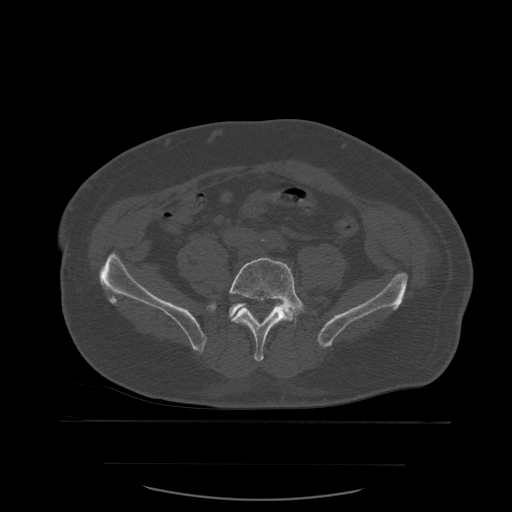
CT including the spine, one axial slice. Bone window (W 1800 / L 400 HU). 512 × 512 image matrix, field of view 479 × 479 mm. Patient age 71 years. Case-level facts recorded for this patient, not image findings: primary cancer: lung; vertebrae with lytic lesions (as recorded): T1, T2, L5, S1.
Structures marked on this image (semi-automatically segmented with operator editing):
- L5 vertebra: bounding box (x1, y1, x2, y2) in pixels: (229, 257, 317, 362)